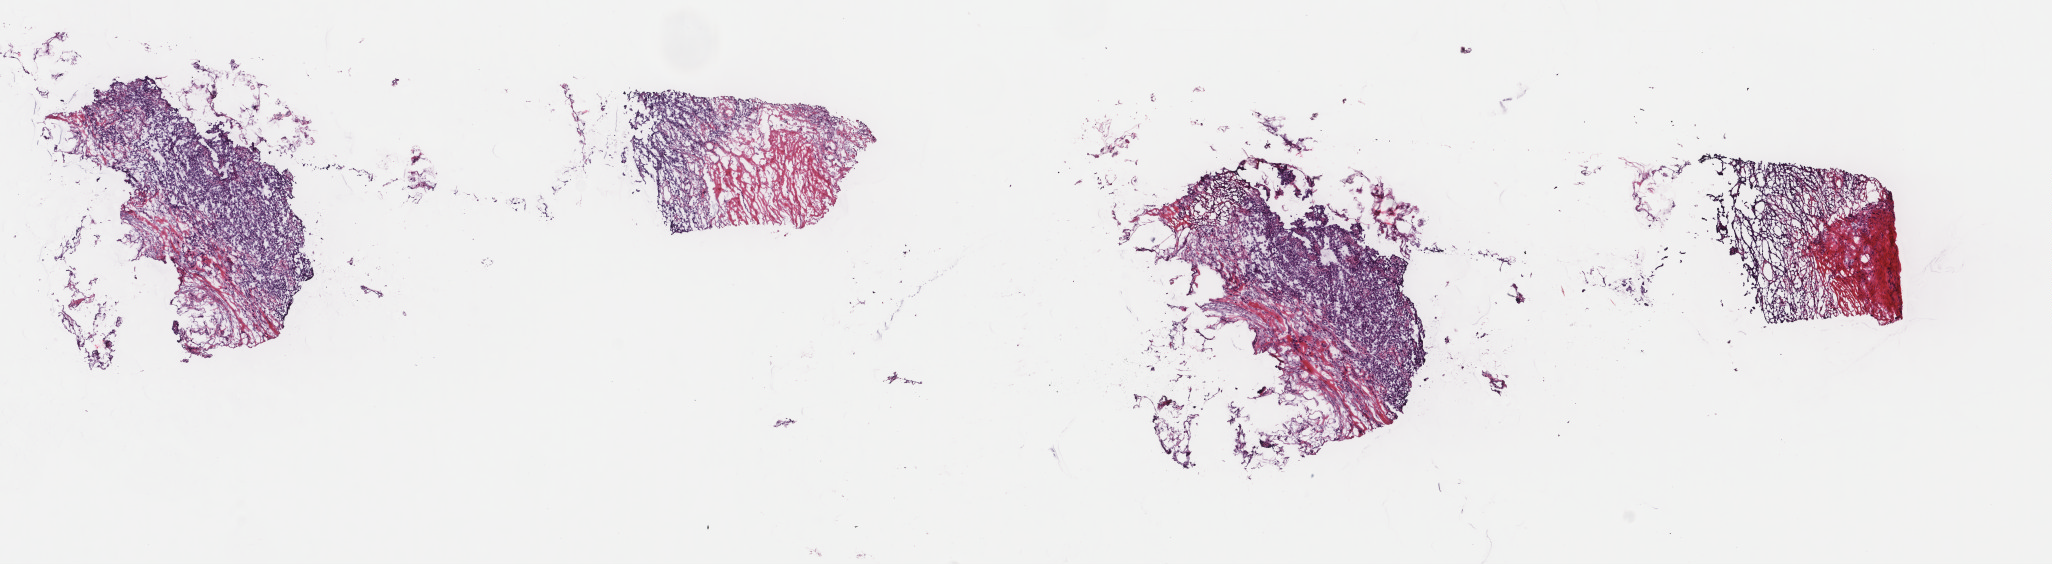
Hematoxylin and eosin (H&E) stained whole-slide image, low-resolution overview of the scanned area, about 16.3 x 4.5 mm; frozen section; metastatic tumour sample. Male, age 42 years at initial diagnosis. Composition of this section per pathologist review: tumour cells 70%, tumour nuclei 85%, normal cells 0%, stromal cells 30%, necrosis 0%. Inflammatory infiltration, as recorded: lymphocyte infiltration 0%, monocyte infiltration 0%, neutrophil infiltration 0%.
This section: metastatic tumour tissue. Patient diagnosis: Malignant melanoma, NOS.